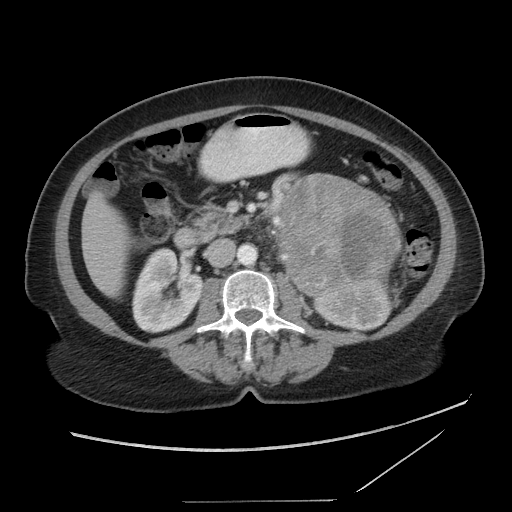
Contrast-enhanced abdominal CT, one axial slice; slice 47 of 86 in the series (ordered by position); intravenous contrast given; soft-tissue window (W 400 / L 40 HU); 512 × 512 image matrix, field of view 398 × 398 mm. Female patient, age 77 years. From the clinical record (not read from this slice): diagnosis: adrenocortical carcinoma; tumour side: left adrenal; tumour size at pathology: 13.1 cm; Ki-67 index: 10 %; stage (as recorded): 3.
Outlined on this slice (semi-automatic segmentation, software-assisted and operator-edited):
- mass: bounding box <281,174,400,297> (left, top, right, bottom; pixels)